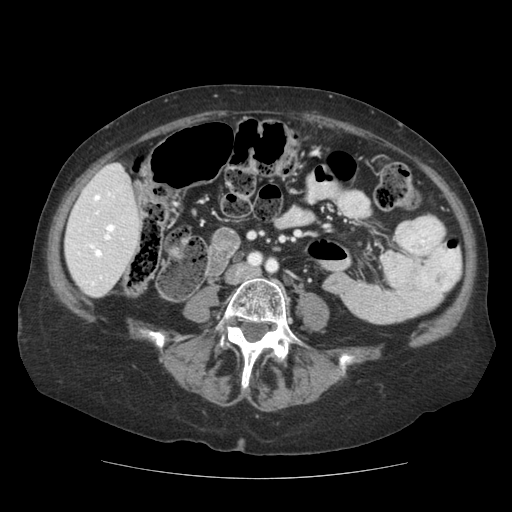
Contrast-enhanced abdominal CT (liver protocol), one axial slice; slice 32 of 111 in the series (ordered by position); reconstruction kernel STANDARD; soft-tissue window (W 400 / L 40 HU); 2.5 mm slice thickness; 512 × 512 image matrix, field of view 360 × 360 mm. Case-level facts recorded for this patient, not image findings: diagnosis: hepatocellular carcinoma (patient treated with transarterial chemoembolisation; whether this scan precedes or follows treatment is not stated here); TNM stage (as recorded): Stage-I; Child-Pugh class: A; tumour differentiation: moderately-poorly differentiated; tumour nodularity: uninodular.
Annotated regions visible in this slice (semi-automatically segmented with operator editing):
- liver parenchyma outside the tumour (the mass and vessels are separate outlines, so this box may not span the whole liver): bounding box (x1, y1, x2, y2) in pixels: (64, 164, 140, 296)
- liver vessels: (78, 192, 115, 286)